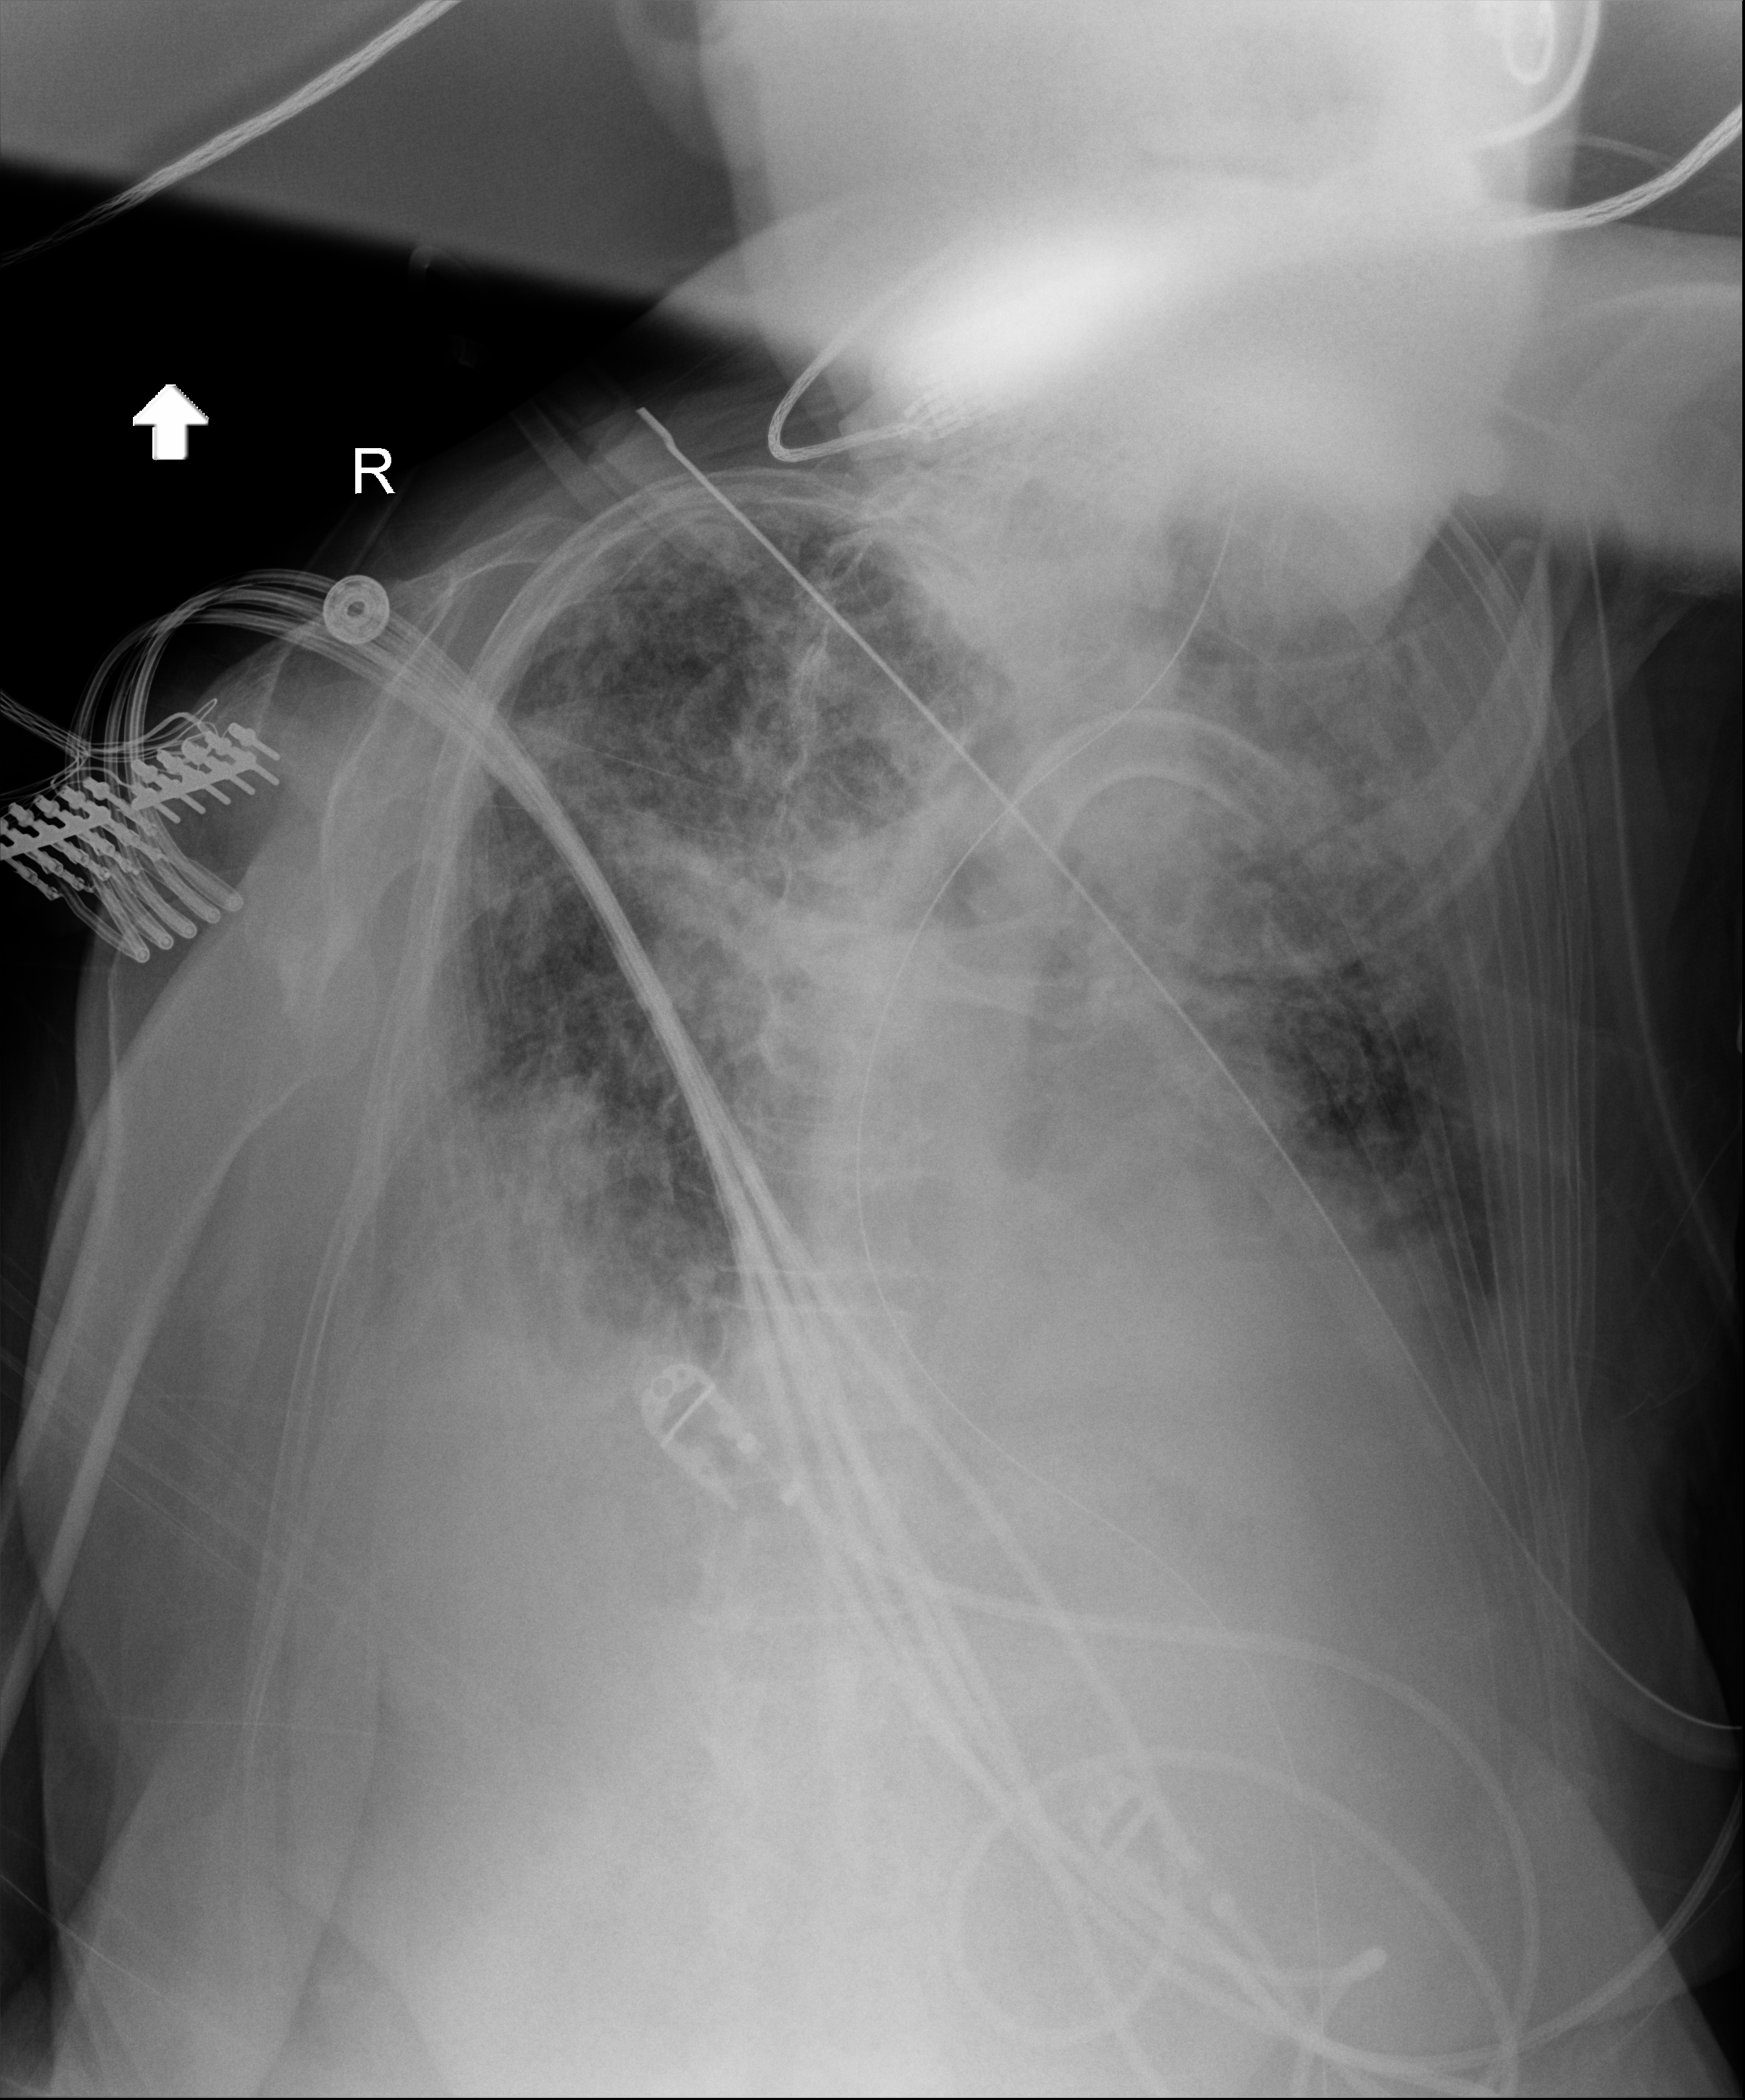
Portable chest radiograph, anteroposterior (AP) projection. Patient hospitalised with COVID-19; female, aged 75–90 years.
Hospital-stay facts (about this admission, not read from this image; timing relative to this image not recorded): diabetes (admission record): no; length of hospital stay: 70 days; admitted to intensive care during this hospital stay: yes.